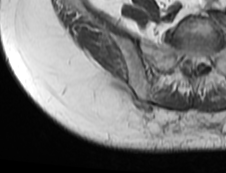
MRI of an extremity soft-tissue mass, one axial slice. Position 57 of 73 along the scan axis. MR volume resampled by the dataset authors to the PET/CT grid (not the native acquisition matrix). 3.27 mm slice thickness. 226 × 173 image matrix. Female patient. Case-level facts recorded for this patient, not image findings: histological type: spindle cell suggestive of myxofibrosarcoma; grade: intermediate; site of the primary tumour: right buttock.
Outlined on this slice (expert contour drawn on MRI and transferred to this co-registered scan by the dataset authors):
- gross tumour volume (mass): box from (x=123, y=94) to (x=181, y=134) px